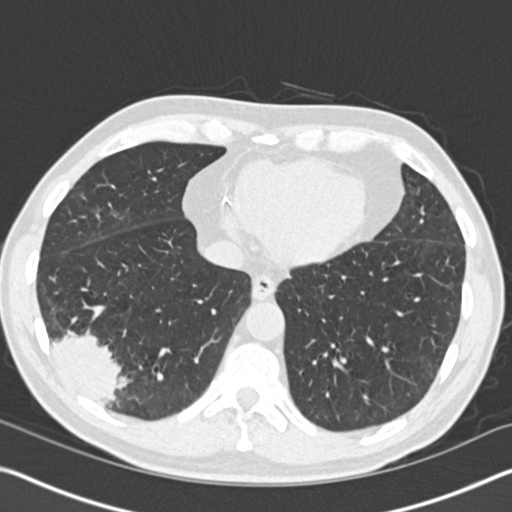
Axial slice from a low-dose chest CT screening exam, first (baseline) screen, lung window (W 1500 / L -600 HU), 2 mm slice thickness, standard (soft-tissue) reconstruction kernel (B30f), 120 kVp, 512 × 512 image matrix, field of view 340 × 340 mm. Male, age 61 years at enrolment.
Expert-annotated lung lesion, bounding box (x1, y1, x2, y2) in pixels: (25, 295, 145, 418). Reader record for this screening exam (exam-level; its link to the box is not recorded): non-calcified nodule or mass ≥4 mm, right lower lobe, 52 × 36 mm, spiculated (stellate) margins, soft tissue attenuation. Official screen result: positive, change unspecified: nodule(s) >= 4 mm or enlarging nodule(s), mass(es), or other non-specific abnormalities suspicious for lung cancer. Later outcome: lung cancer diagnosed 392 days after this screen (after the second annual screen) — bronchiolo-alveolar adenocarcinoma, NOS, right lower lobe, moderately differentiated (G2), stage IIIB (AJCC 6th edition), 90 mm at pathology.